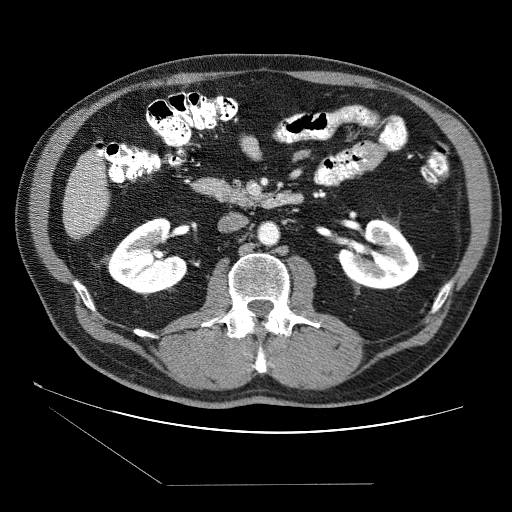
Contrast-enhanced abdominal CT (liver protocol), one axial slice. Slice 11 of 87 in the series (ordered by position). Reconstruction kernel STANDARD. Soft-tissue window (W 400 / L 40 HU). 512 × 512 image matrix. From the clinical record (not read from this slice): diagnosis: hepatocellular carcinoma (patient treated with transarterial chemoembolisation; whether this scan precedes or follows treatment is not stated here); TNM stage (as recorded): Stage-II; Child-Pugh class: B; tumour differentiation: no biopsy; tumour size: 2.6 cm.
Structures marked on this image (semi-automatic segmentation, software-assisted and operator-edited):
- liver parenchyma outside the tumour (the mass and vessels are separate outlines, so this box may not span the whole liver): bounding box <64,152,110,236> (left, top, right, bottom; pixels)
- liver vessels: <70,171,96,219>